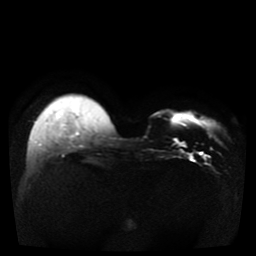
Breast MRI, one axial slice. Diffusion-weighted series; image 2 of 4 stored at this slice position (different b-values; order by instance number). 1.5 T. 5 mm slice thickness. 256 × 256 image matrix, field of view 330 × 330 mm. Female patient.
Annotated regions visible in this slice (expert manual segmentation):
- tumour on diffusion-weighted imaging: bounding box (x1, y1, x2, y2) in pixels: (174, 140, 180, 146)